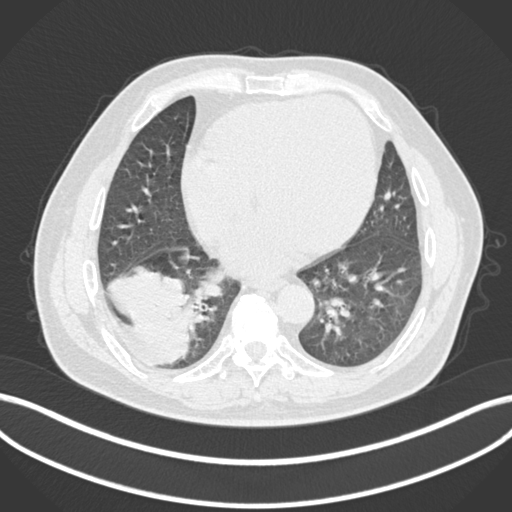
Chest CT, one axial slice; slice 54 of 200 in the series (ordered by position); 120 kVp; lung window (W 1500 / L -600 HU); 1 mm slice thickness; 512 × 512 image matrix. Male patient, age 59 years.
Outlined on this slice (rectangle marked by the reading radiologist):
- lung tumour (recorded histology: adenocarcinoma): box from (x=105, y=259) to (x=200, y=364) px